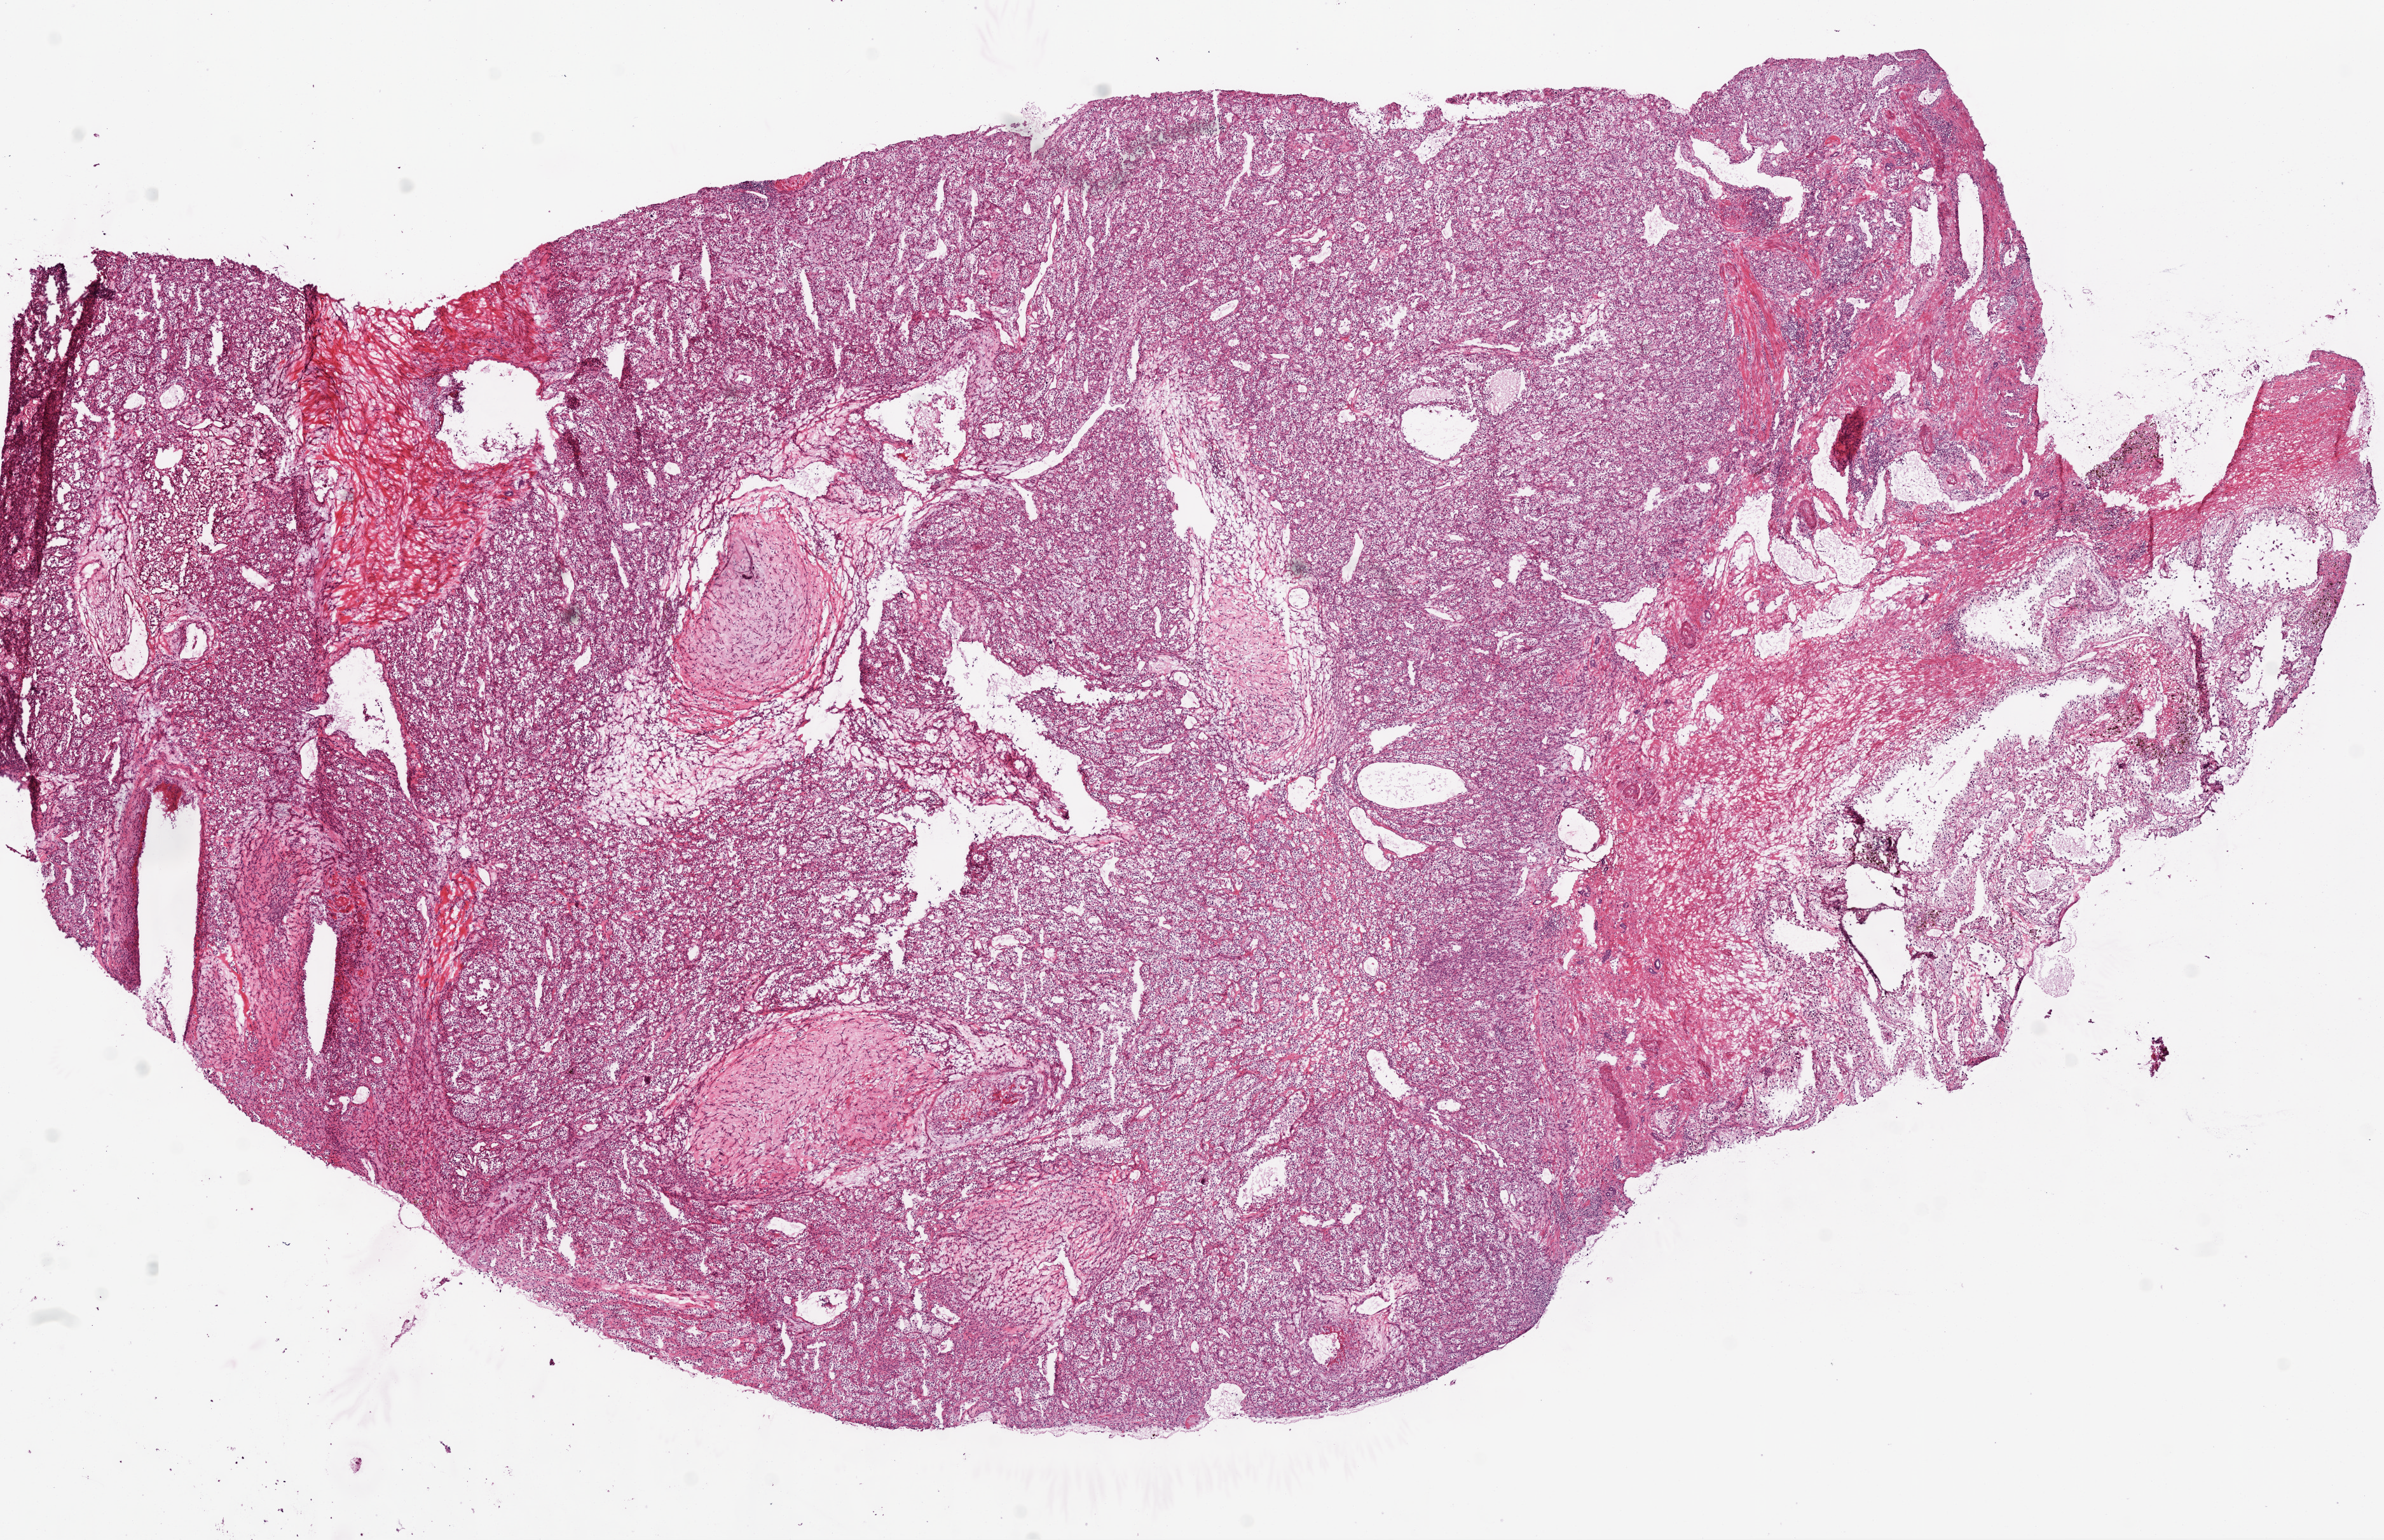
Digitized Hematoxylin and eosin (H&E) stained tissue section (whole slide) — whole scanned area (about 15.0 x 9.7 mm, slide scanned at 20x) shown as a low-resolution overview. Frozen section. Kidney, primary tumour sample. Male patient; age at initial diagnosis 69 years. Slide review estimates, as recorded: tumour cells 70%, tumour nuclei 80%.
Histologic diagnosis: Clear cell adenocarcinoma, NOS.